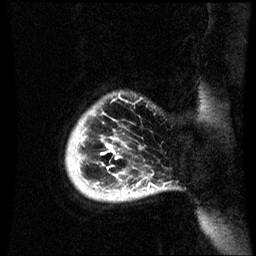
Breast MRI (dynamic contrast-enhanced), one sagittal slice. Slice 6 of 60 in the series (ordered by position). Dynamic contrast-enhanced series, image 2 of 3 at this slice position (ordered by acquisition). 1.5 T. TE 4.2 ms, TR 8.9 ms. 256 × 256 image matrix, field of view 220 × 220 mm. Patient: female, 35 years. Case-level facts recorded for this patient, not image findings: setting: breast cancer imaged before/during neoadjuvant chemotherapy; receptor status: HR-positive, HER2-negative.
Structures marked on this image (semi-automatic segmentation, software-assisted and operator-edited):
- analysis volume of interest (the breast-tissue region the enhancement analysis was run in; not a lesion): bounding box [x1, y1, x2, y2] px = [66, 94, 164, 203]
- tumour enhancement mask (voxels above the 70 % enhancement threshold inside the analysis volume of interest): [101, 138, 120, 199]